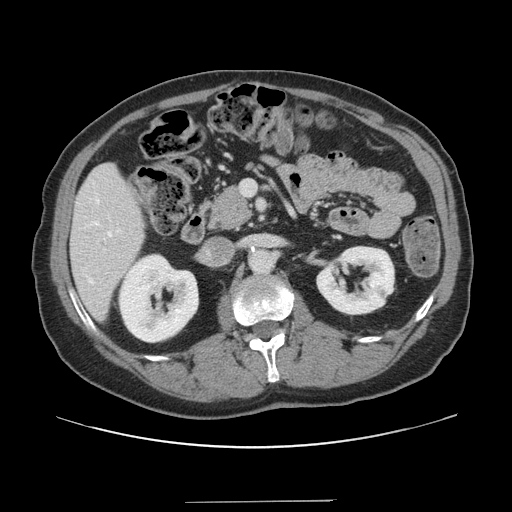
Contrast-enhanced abdominal CT, one axial slice. Position 65 of 151 along the scan axis. 120 kVp. Intravenous contrast given. Soft-tissue window (W 400 / L 40 HU). 2.5 mm slice thickness. 512 × 512 image matrix. Male patient, age 63 years. Case-level facts recorded for this patient, not image findings: diagnosis: colorectal cancer liver metastases, imaged before liver resection; multiple liver metastases: no; largest metastasis: 2.1 cm; disease in both lobes: no.
Annotated regions visible in this slice (outlined manually by an expert reader):
- hepatic veins: bounding box [x1, y1, x2, y2] px = [89, 231, 112, 284]
- liver: [72, 165, 144, 318]
- planned liver remnant (the part of the liver to remain after resection): [72, 165, 145, 319]
- portal vein (with intrahepatic branches): [104, 180, 255, 251]